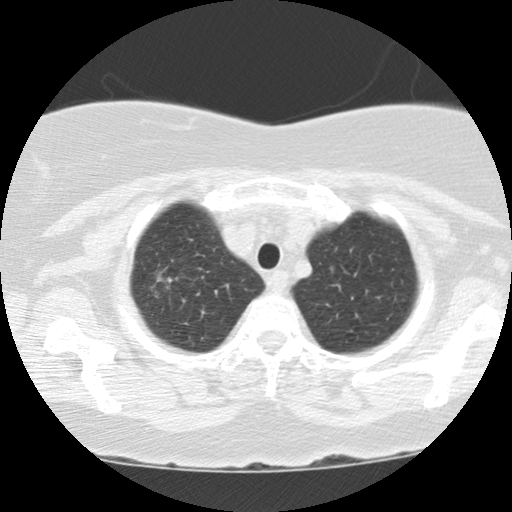
Low-dose screening chest CT, axial slice, baseline screening round, lung window (W 1500 / L -600 HU), 2.5 mm slice thickness, standard (soft-tissue) reconstruction kernel (STANDARD), slice 13 of 112 in the series. Female, age 67 years at enrolment. Former smoker at enrolment.
- Expert-annotated lung lesion, bounding box (x1, y1, x2, y2) in pixels: (129, 250, 198, 311).
- The screening reader recorded 3 non-calcified nodules or masses ≥4 mm on this exam (right upper lobe, right lower lobe, right upper lobe); which of them this box marks is not recorded.
- Later outcome: lung cancer diagnosed 441 days after this screen (after the second annual screen) — adenocarcinoma with mixed subtypes, right upper lobe, poorly differentiated (G3), stage IA (AJCC 6th edition), 30 mm at pathology.